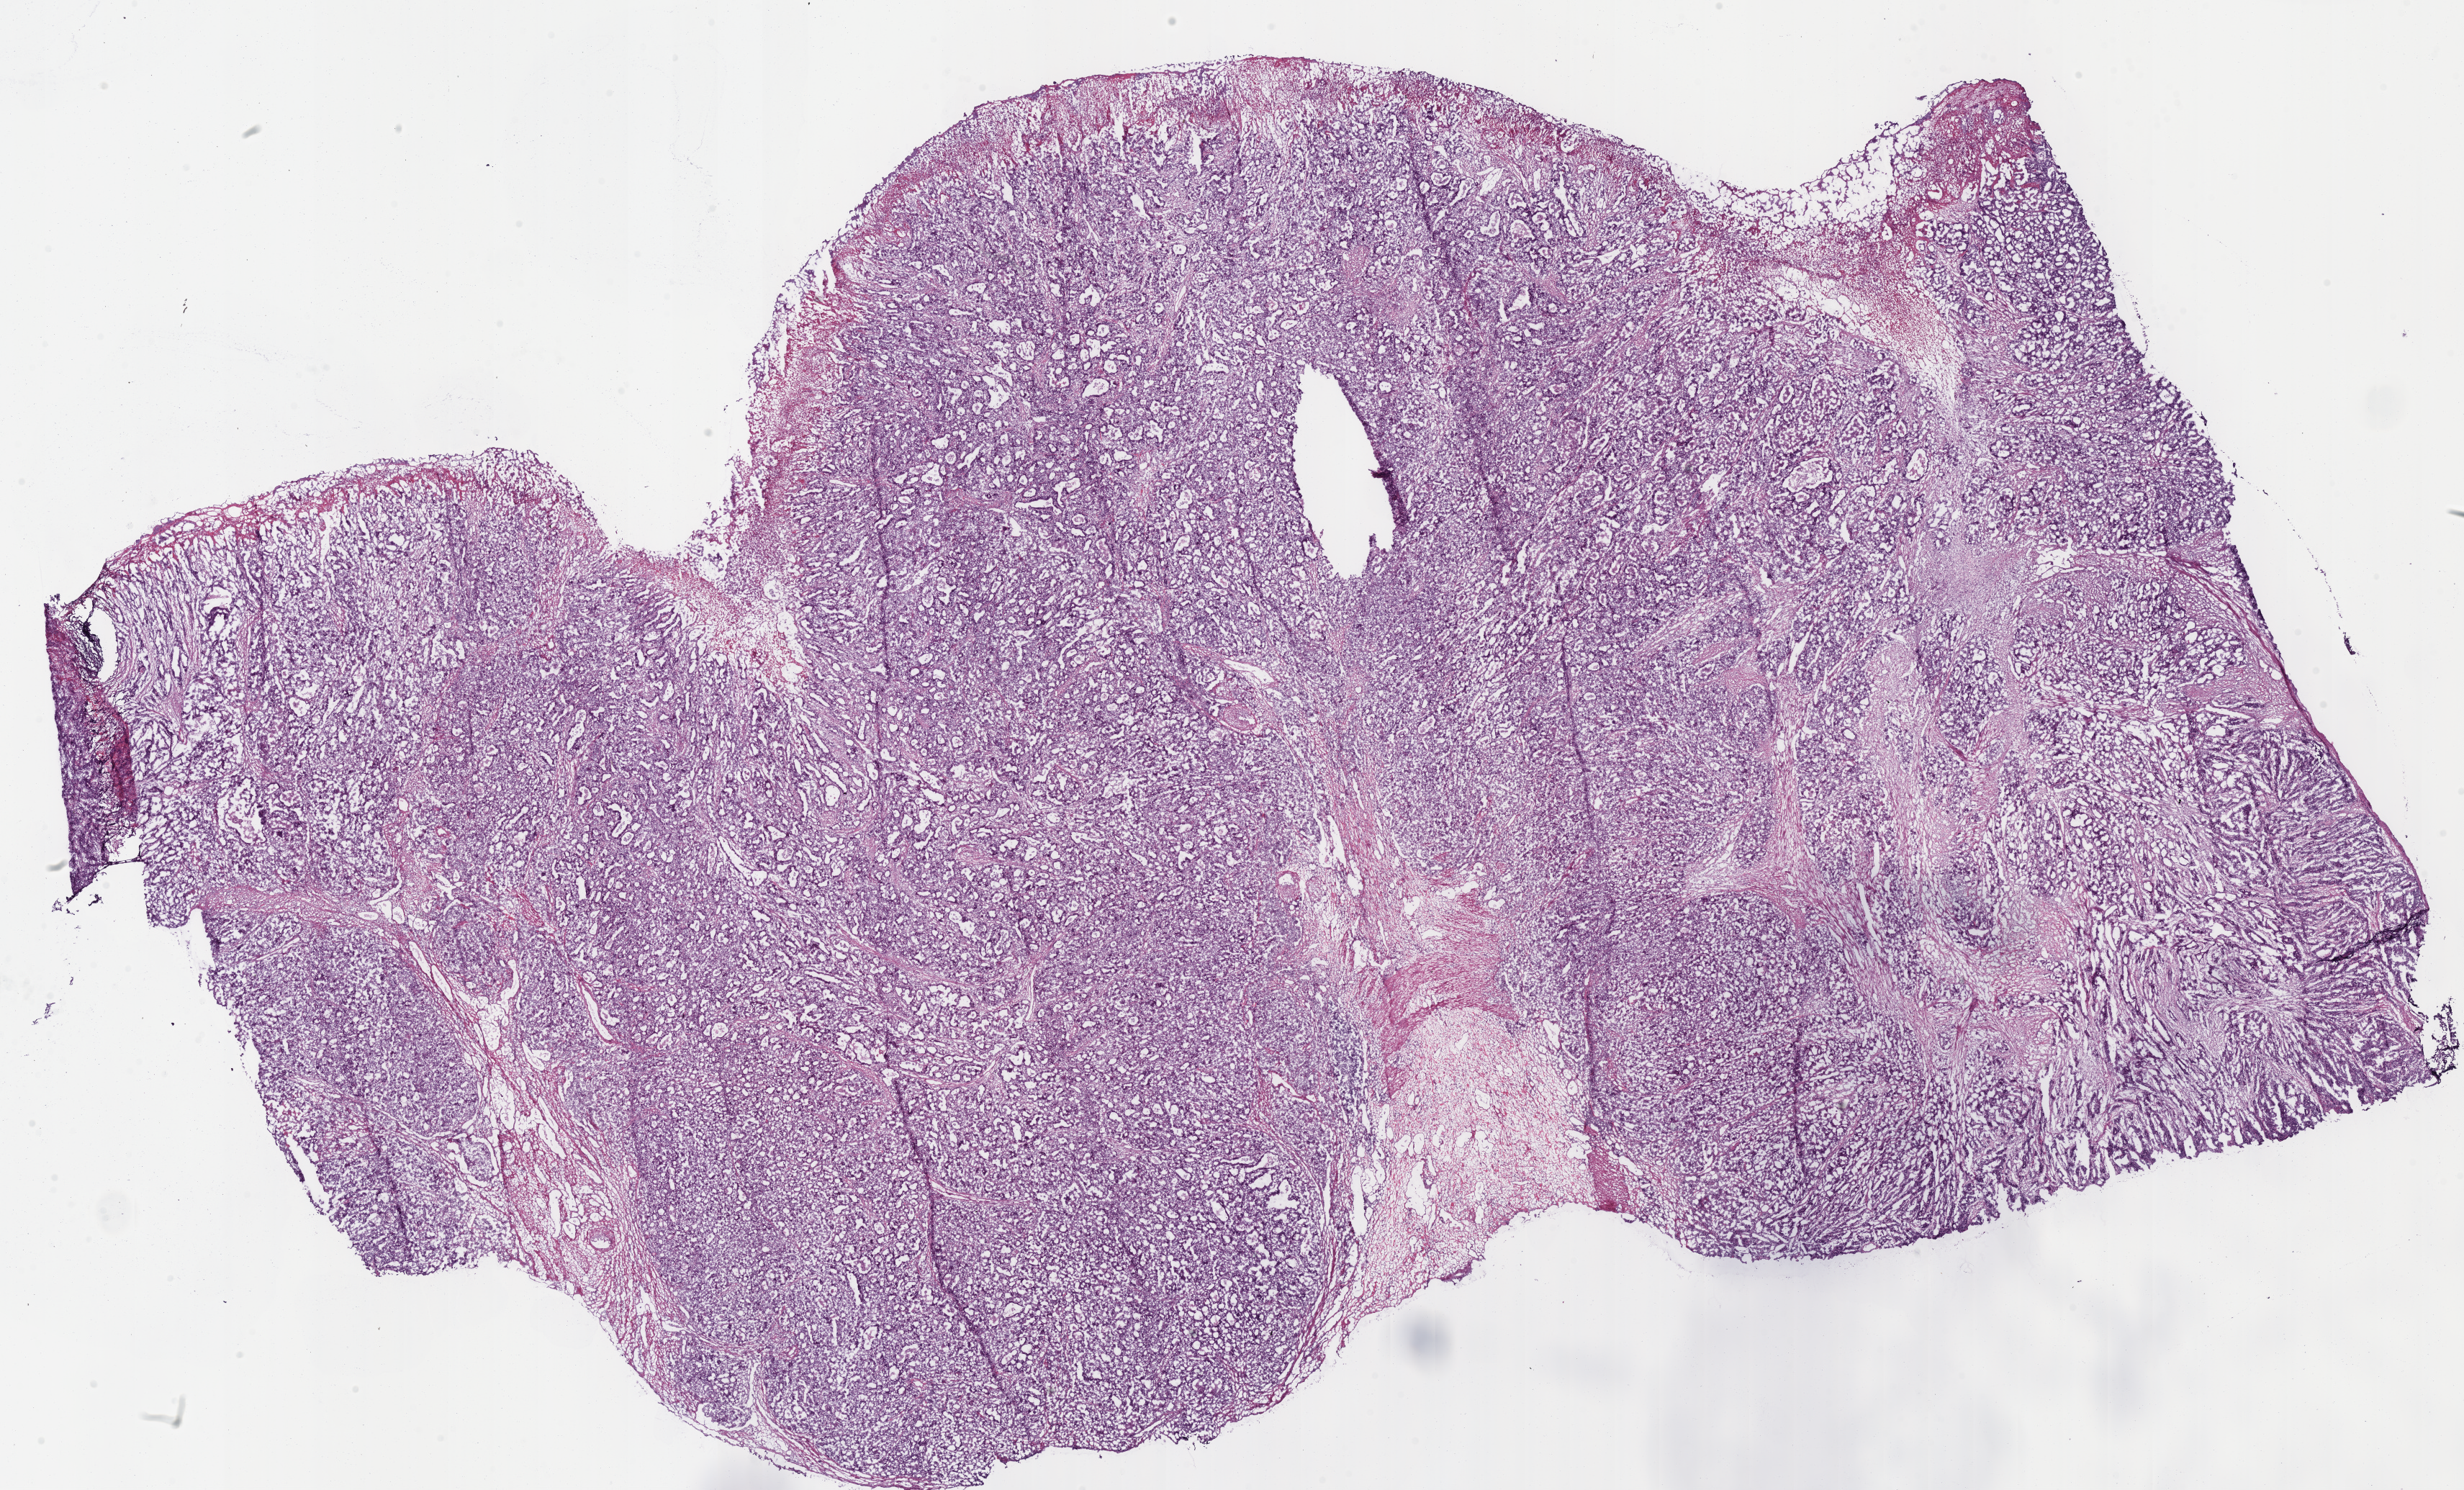
Hematoxylin and eosin (H&E) stained whole-slide image, whole scanned area (about 26.9 x 16.3 mm, slide scanned at 40x) shown as a low-resolution overview, frozen section from the bottom of the tissue portion, sample: primary tumour, stomach. Male patient; age at initial diagnosis 66 years. Pathologist review of this section (percent, as recorded): tumour cells 90%, tumour nuclei 80%.
Histologic diagnosis: Adenocarcinoma, intestinal type (fundus of stomach).